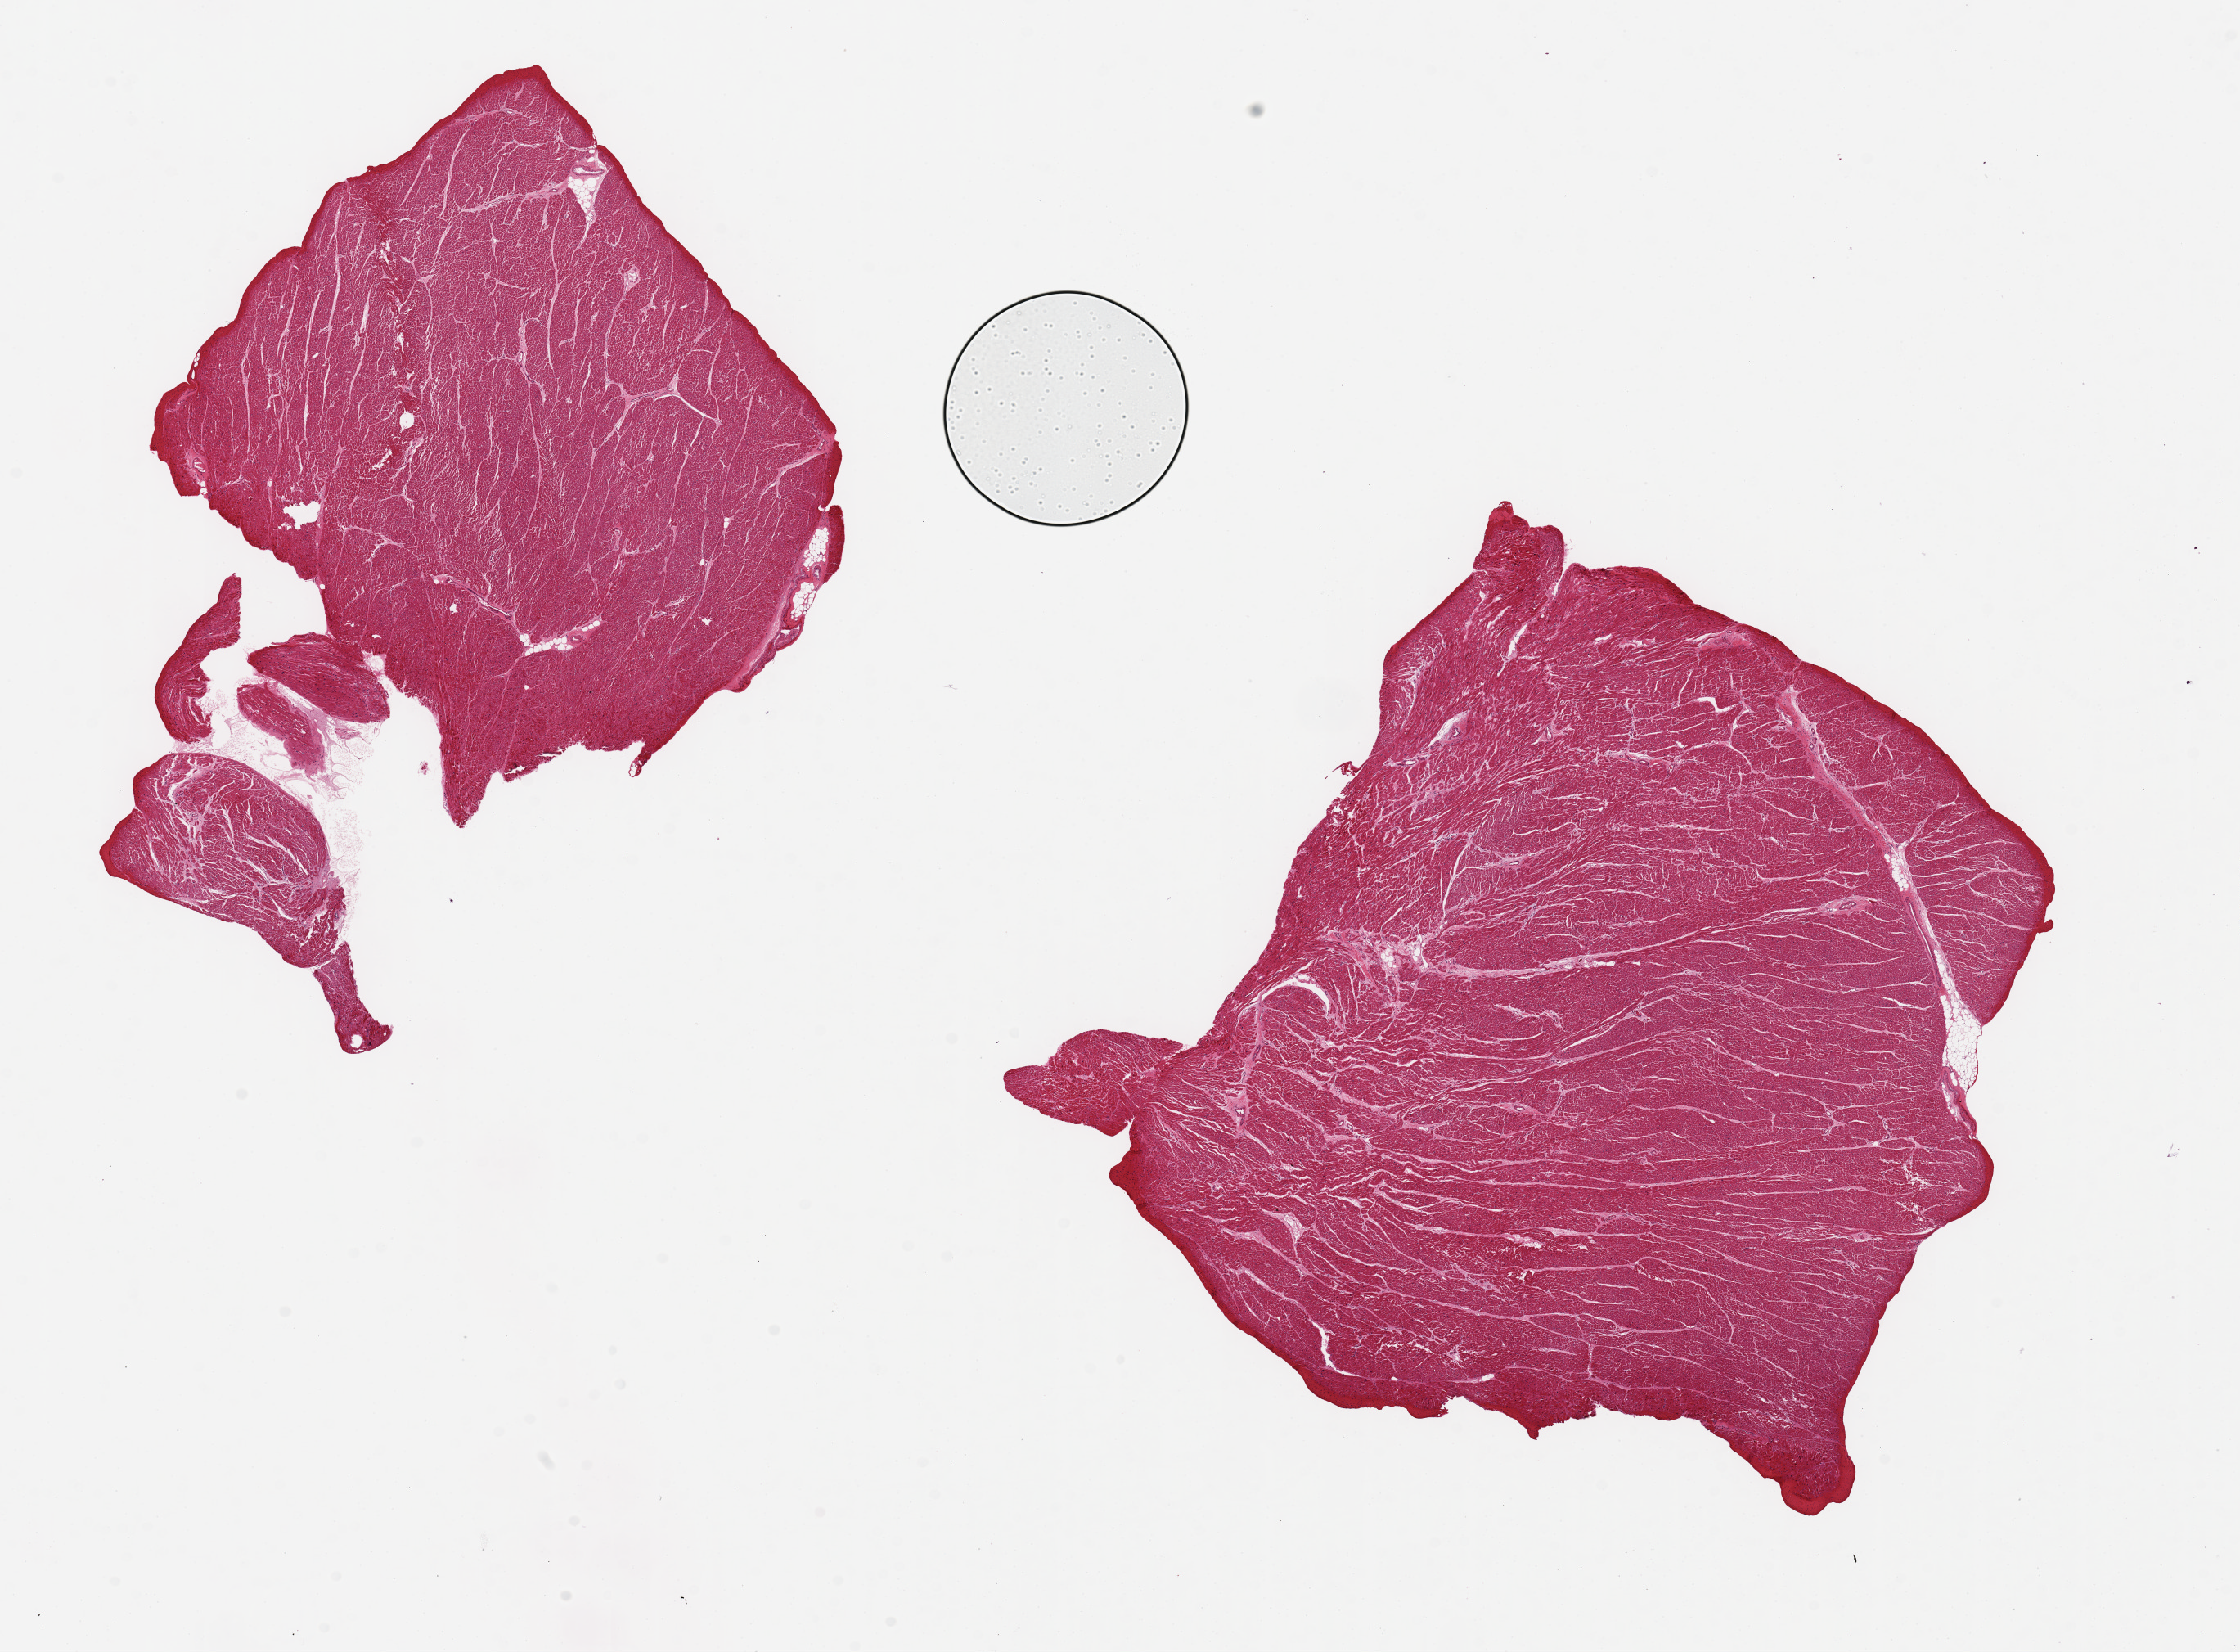
Whole-slide image, hematoxylin and eosin (H&E) stain, brightfield, a low-resolution overview of the entire scanned area, about 21.7 x 16.0 mm (acquisition: 20x scan), PAXgene-fixed paraffin-embedded (PFPE) section, sampled site (target tissue): heart, donor tissue sample. Male donor.
• pathologist's review note for this sample: 2 pieces ?ventricle 6x6 mm, no significant ischemic changes